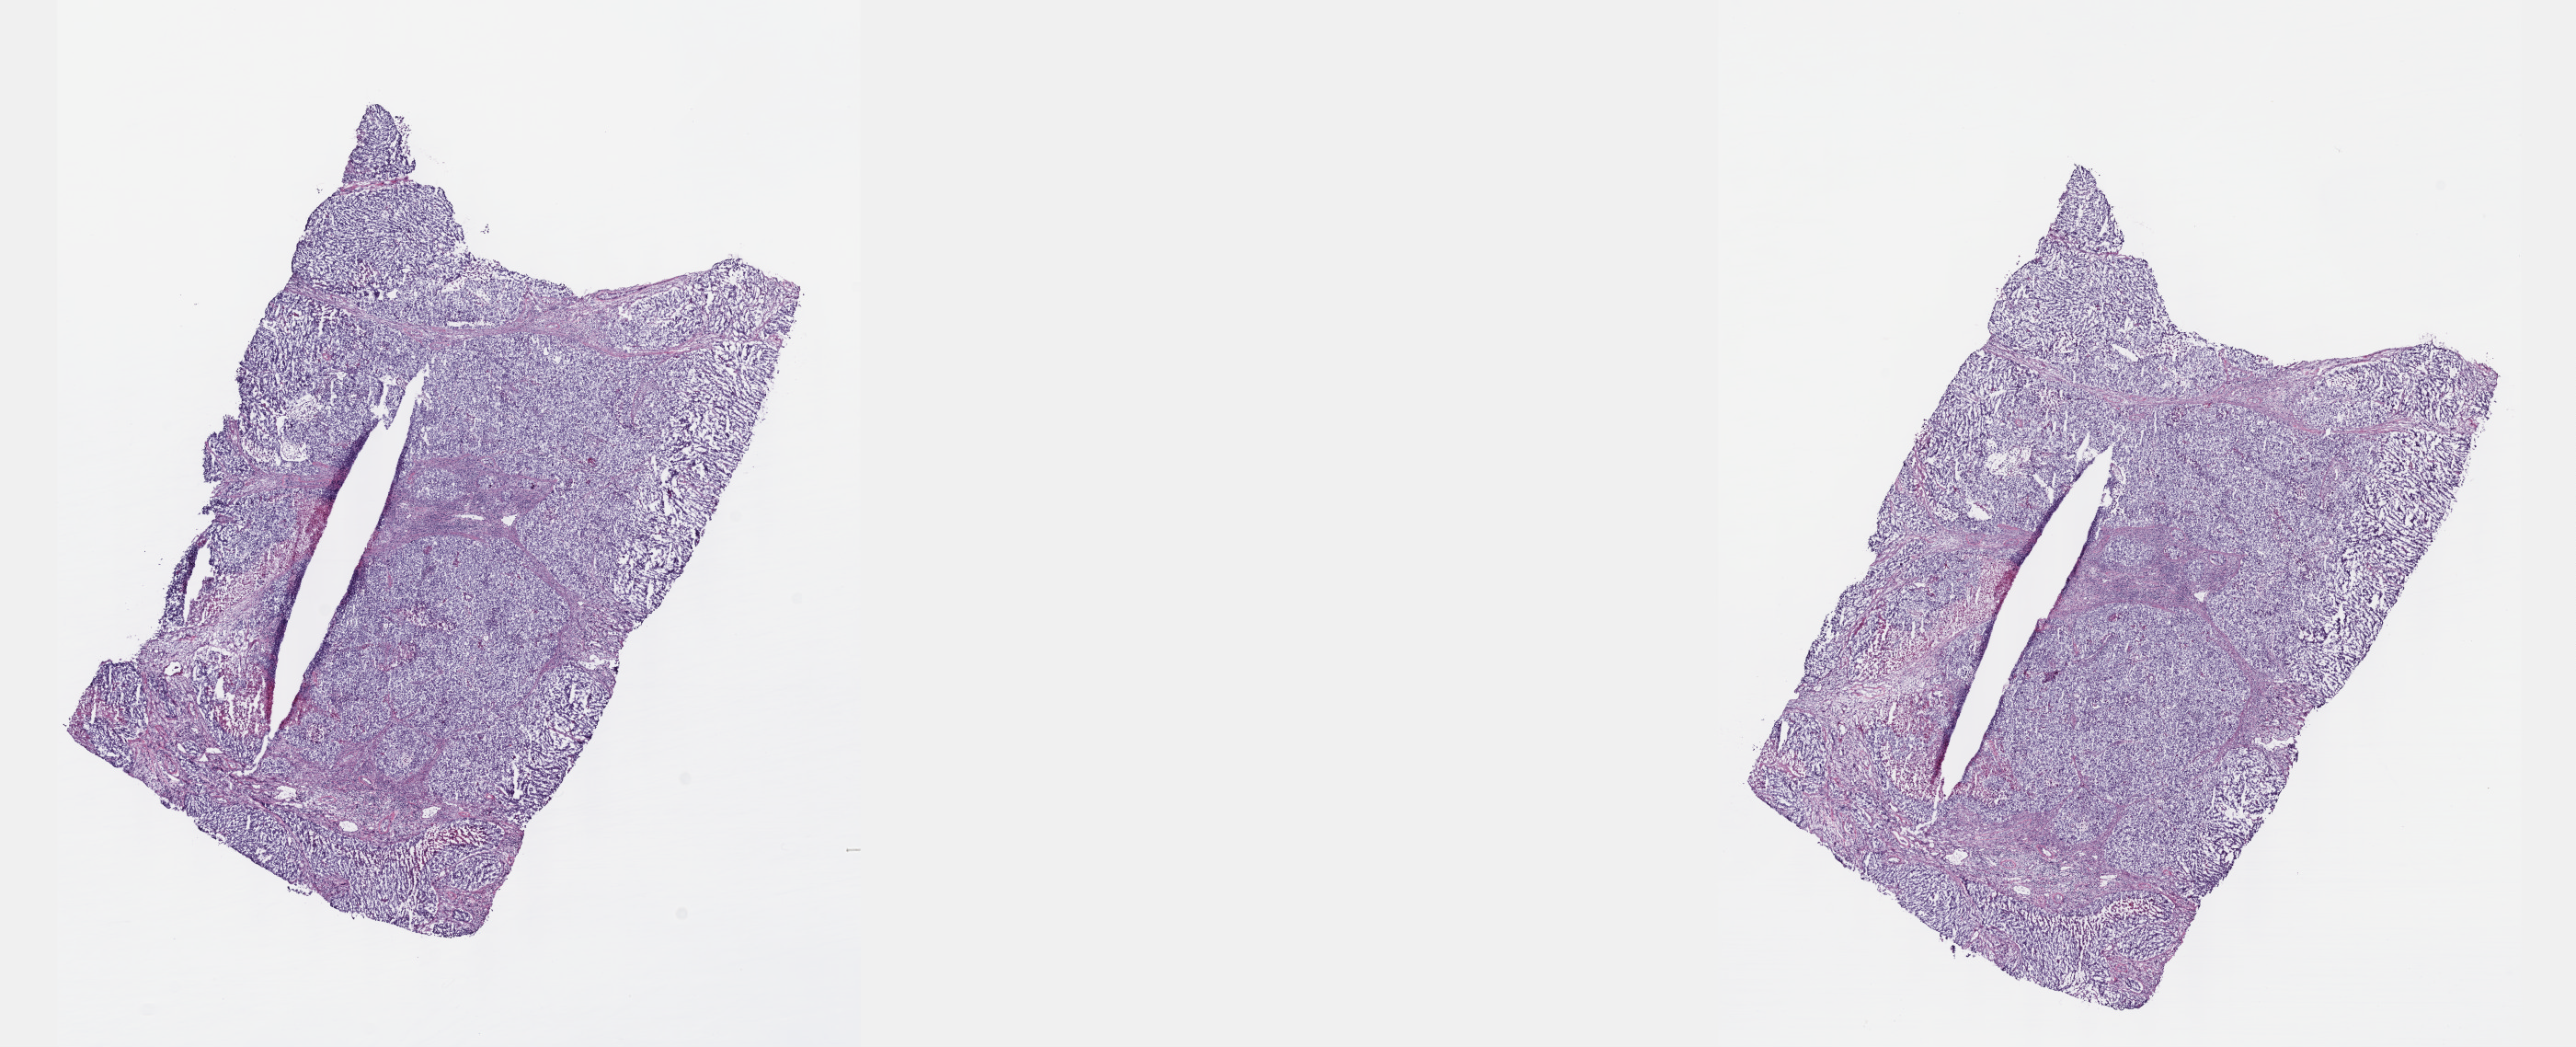
Digitized H&E tissue section (whole slide) — shown as a low-resolution overview of the whole scanned area (about 22.6 x 9.2 mm, from a 40x scan), frozen section, testis, primary tumour sample. Patient: male, age at initial diagnosis 41 years. Slide review estimates, as recorded: tumour cells 90%, tumour nuclei 90%, normal cells 0%, stromal cells 5%, necrosis 5%. Infiltration values recorded for this section: lymphocyte infiltration 40%, monocyte infiltration 20%, neutrophil infiltration 20%.
AJCC pathologic stage: IIIB (6th edition). Pathologic diagnosis: Embryonal carcinoma, NOS. Laterality: left.